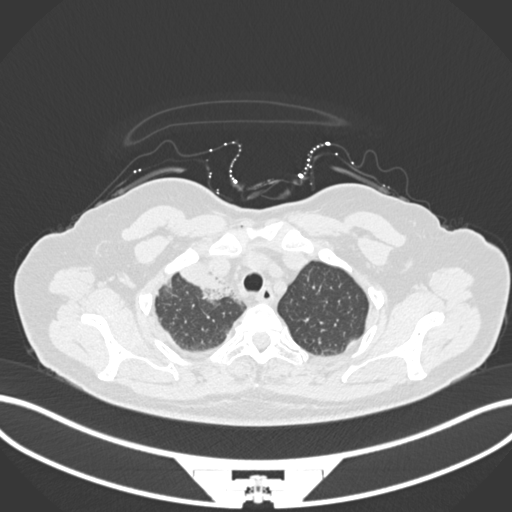
Chest CT, one axial slice. Slice 144 of 172 in the series (ordered by position). Reconstruction kernel B30f. Lung window (W 1500 / L -600 HU). 512 × 512 image matrix. Patient: female, 52 years. Case-level facts recorded for this patient, not image findings: clinical TNM (as recorded): T3 N1 M1.
Outlined on this slice (bounding box drawn by a radiologist):
- lung tumour (recorded histology: adenocarcinoma): bounding box <180,264,228,300> (left, top, right, bottom; pixels)